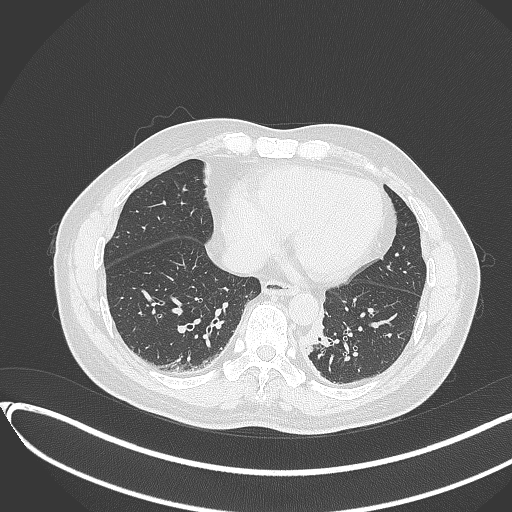
Chest CT, one axial slice. Slice 102 of 417 in the series (ordered by position). Reconstruction kernel B70f. 120 kVp. Lung window (W 1500 / L -600 HU). 1 mm slice thickness. 512 × 512 image matrix, field of view 400 × 400 mm. Patient: male, 54 years. Case-level facts recorded for this patient, not image findings: clinical TNM (as recorded): T3 N0 M0.
Annotated regions visible in this slice (bounding box drawn by a radiologist):
- lung tumour (recorded histology: squamous cell carcinoma): bounding box [x1, y1, x2, y2] px = [301, 307, 331, 351]